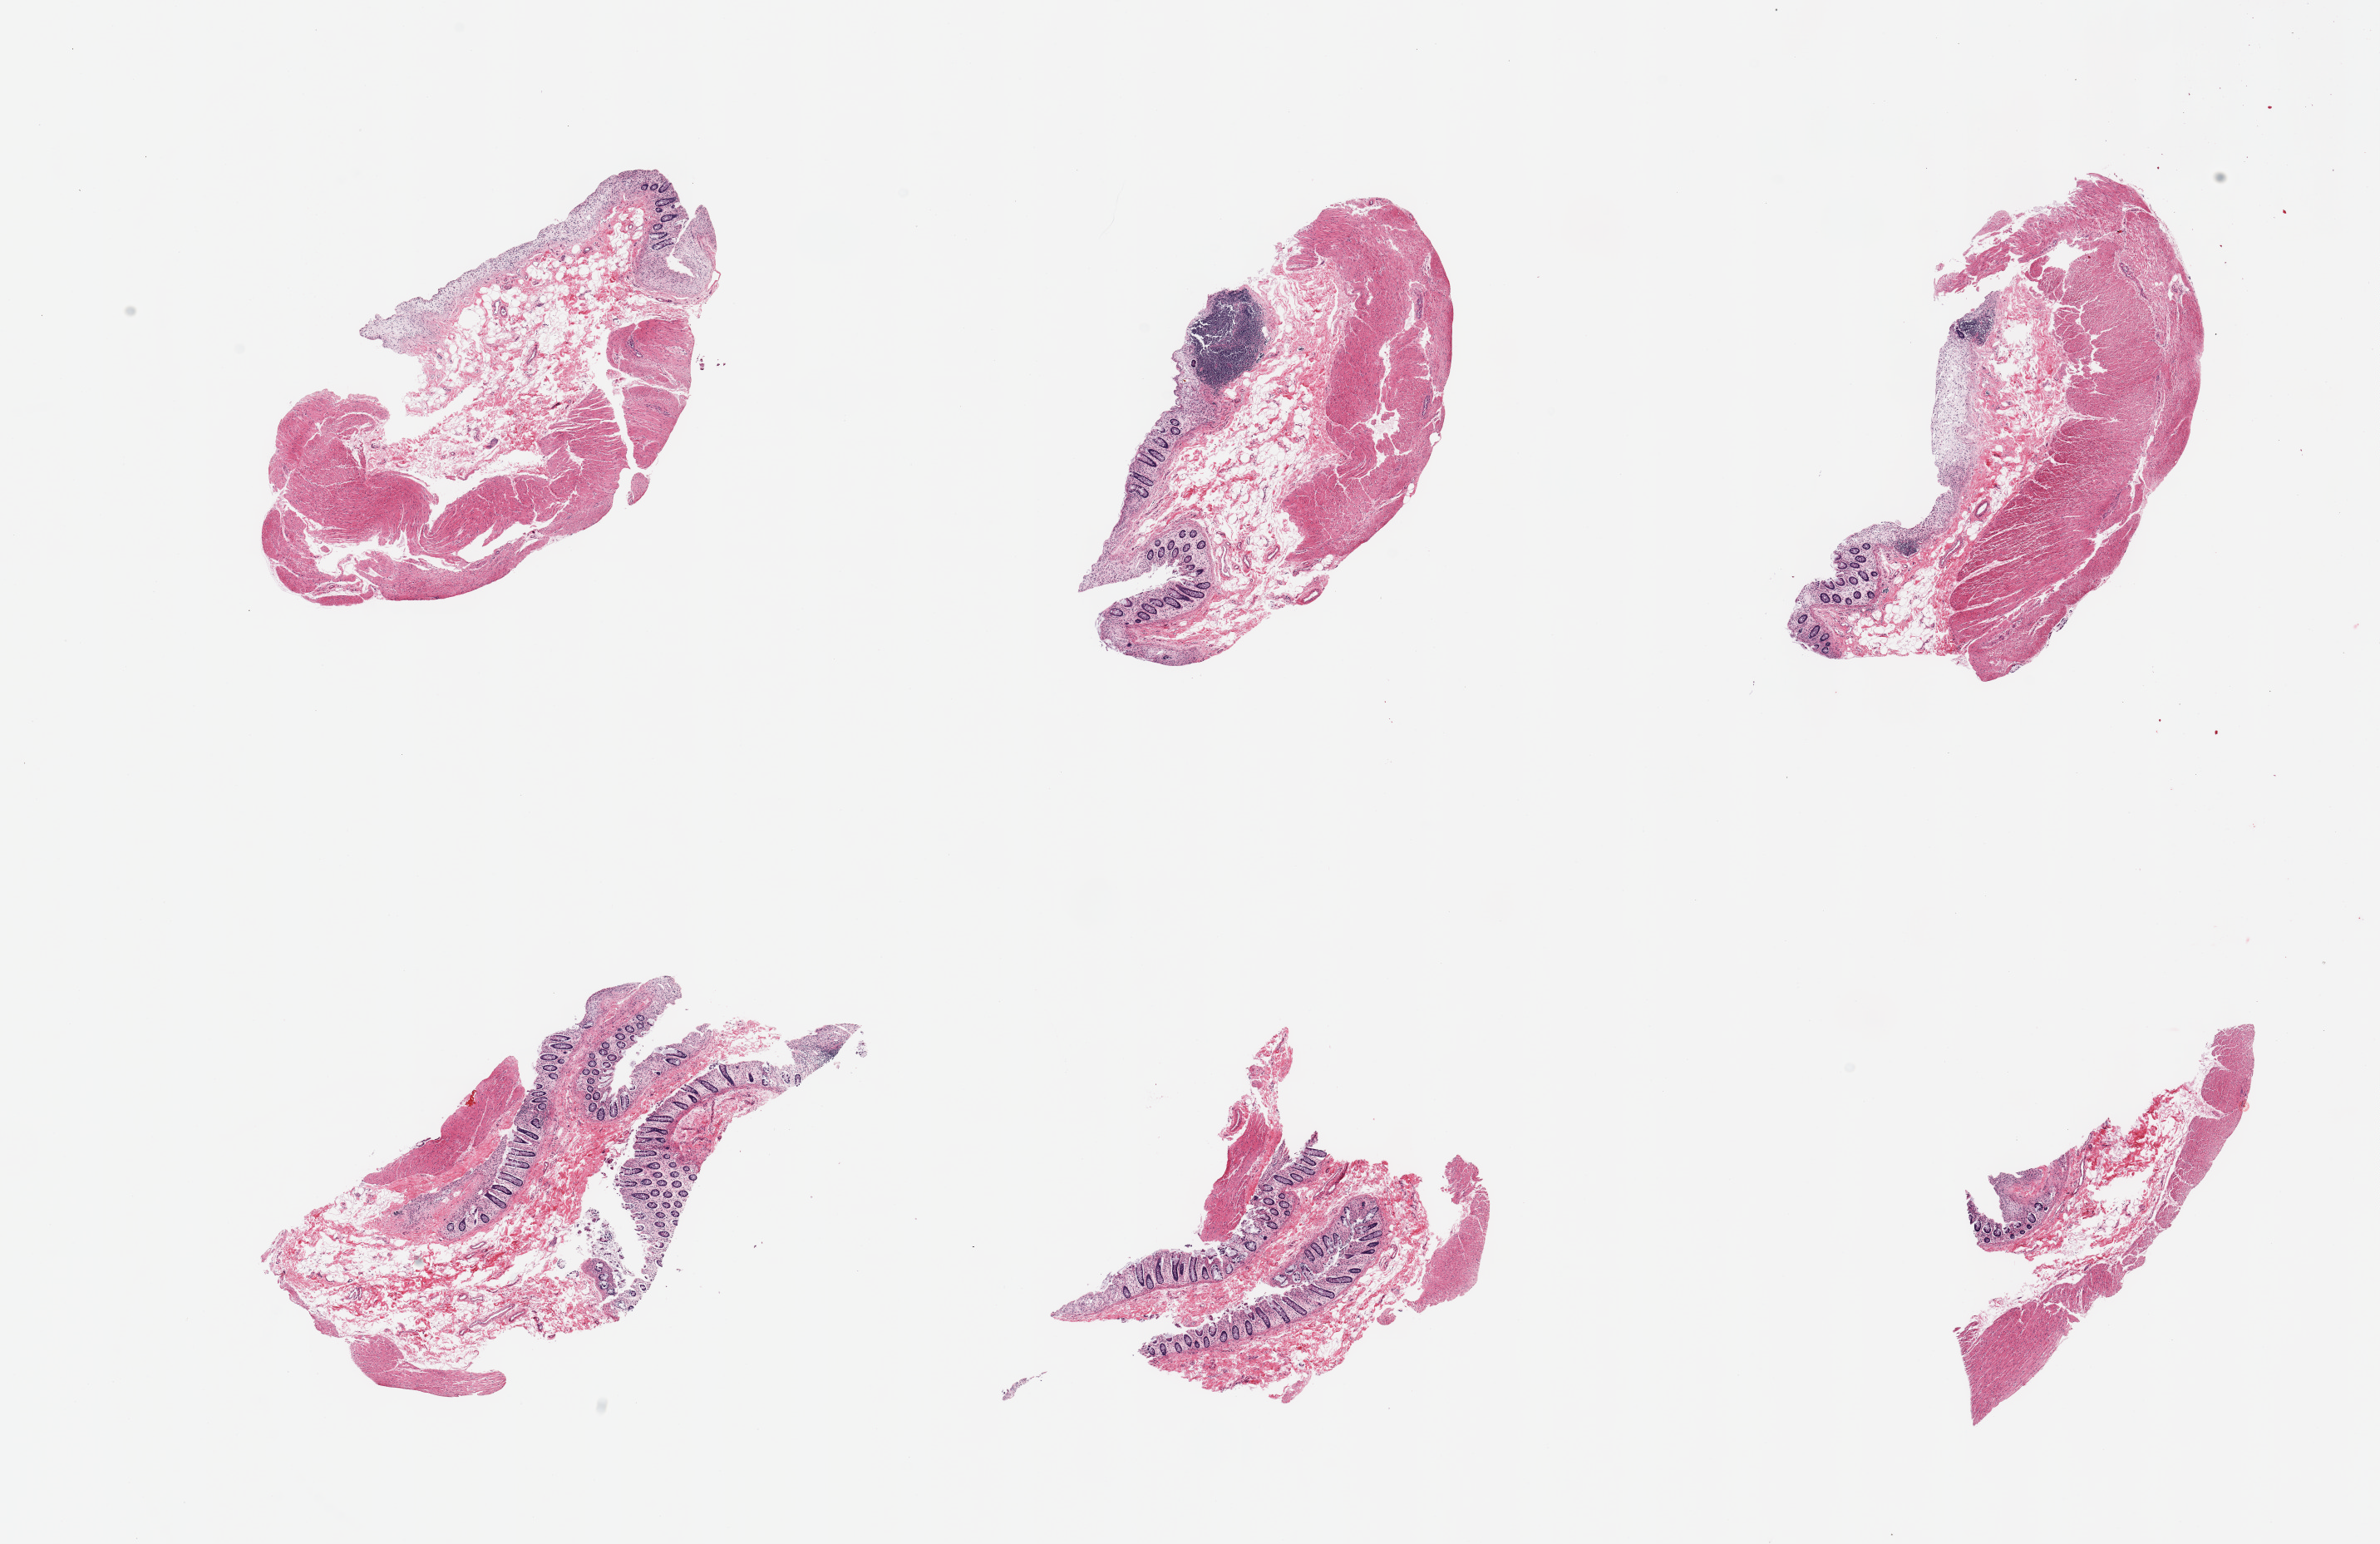
Whole-slide image, hematoxylin and eosin (H&E) stain, brightfield, shown as a low-resolution overview of the whole scanned area (about 22.6 x 14.7 mm, slide scanned at 20x). Donor sex: female.
Specimen: PAXgene-fixed paraffin-embedded (PFPE) section; sampled site (target tissue): sigmoid colon; donor tissue sample.